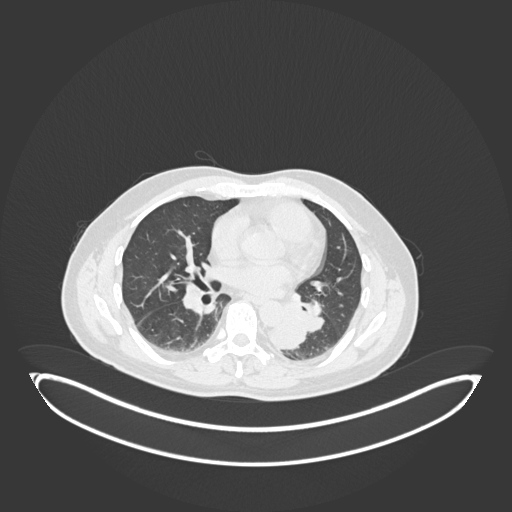
Chest CT, one axial slice. 120 kVp. Lung window (W 1500 / L -600 HU). 1 mm slice thickness. 512 × 512 image matrix, field of view 500 × 500 mm. Patient: male, 54 years. Case-level facts recorded for this patient, not image findings: clinical TNM (as recorded): T3 N0 M0.
Outlined on this slice (rectangle marked by the reading radiologist):
- lung tumour (recorded histology: squamous cell carcinoma): bounding box [x1, y1, x2, y2] px = [264, 300, 308, 353]